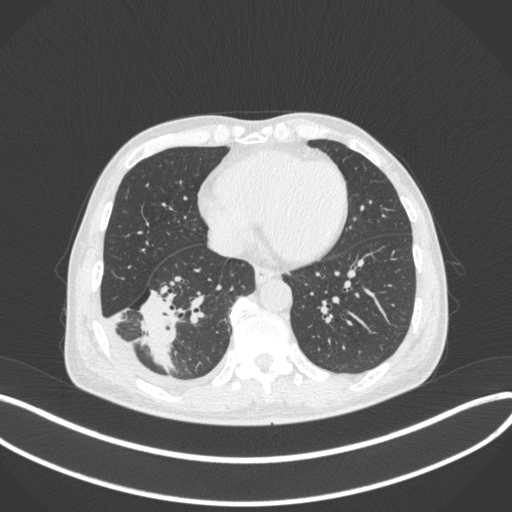
Chest CT, one axial slice. Position 130 of 385 along the scan axis. Reconstruction kernel B31f. 120 kVp. Lung window (W 1500 / L -600 HU). 1 mm slice thickness. 512 × 512 image matrix, field of view 400 × 400 mm. Male patient, age 64 years. Case-level facts recorded for this patient, not image findings: clinical TNM (as recorded): T3 N0 M0; histopathological grade: G2-3.
Structures marked on this image (rectangle marked by the reading radiologist):
- lung tumour (recorded histology: adenocarcinoma): bounding box [x1, y1, x2, y2] px = [137, 281, 181, 373]